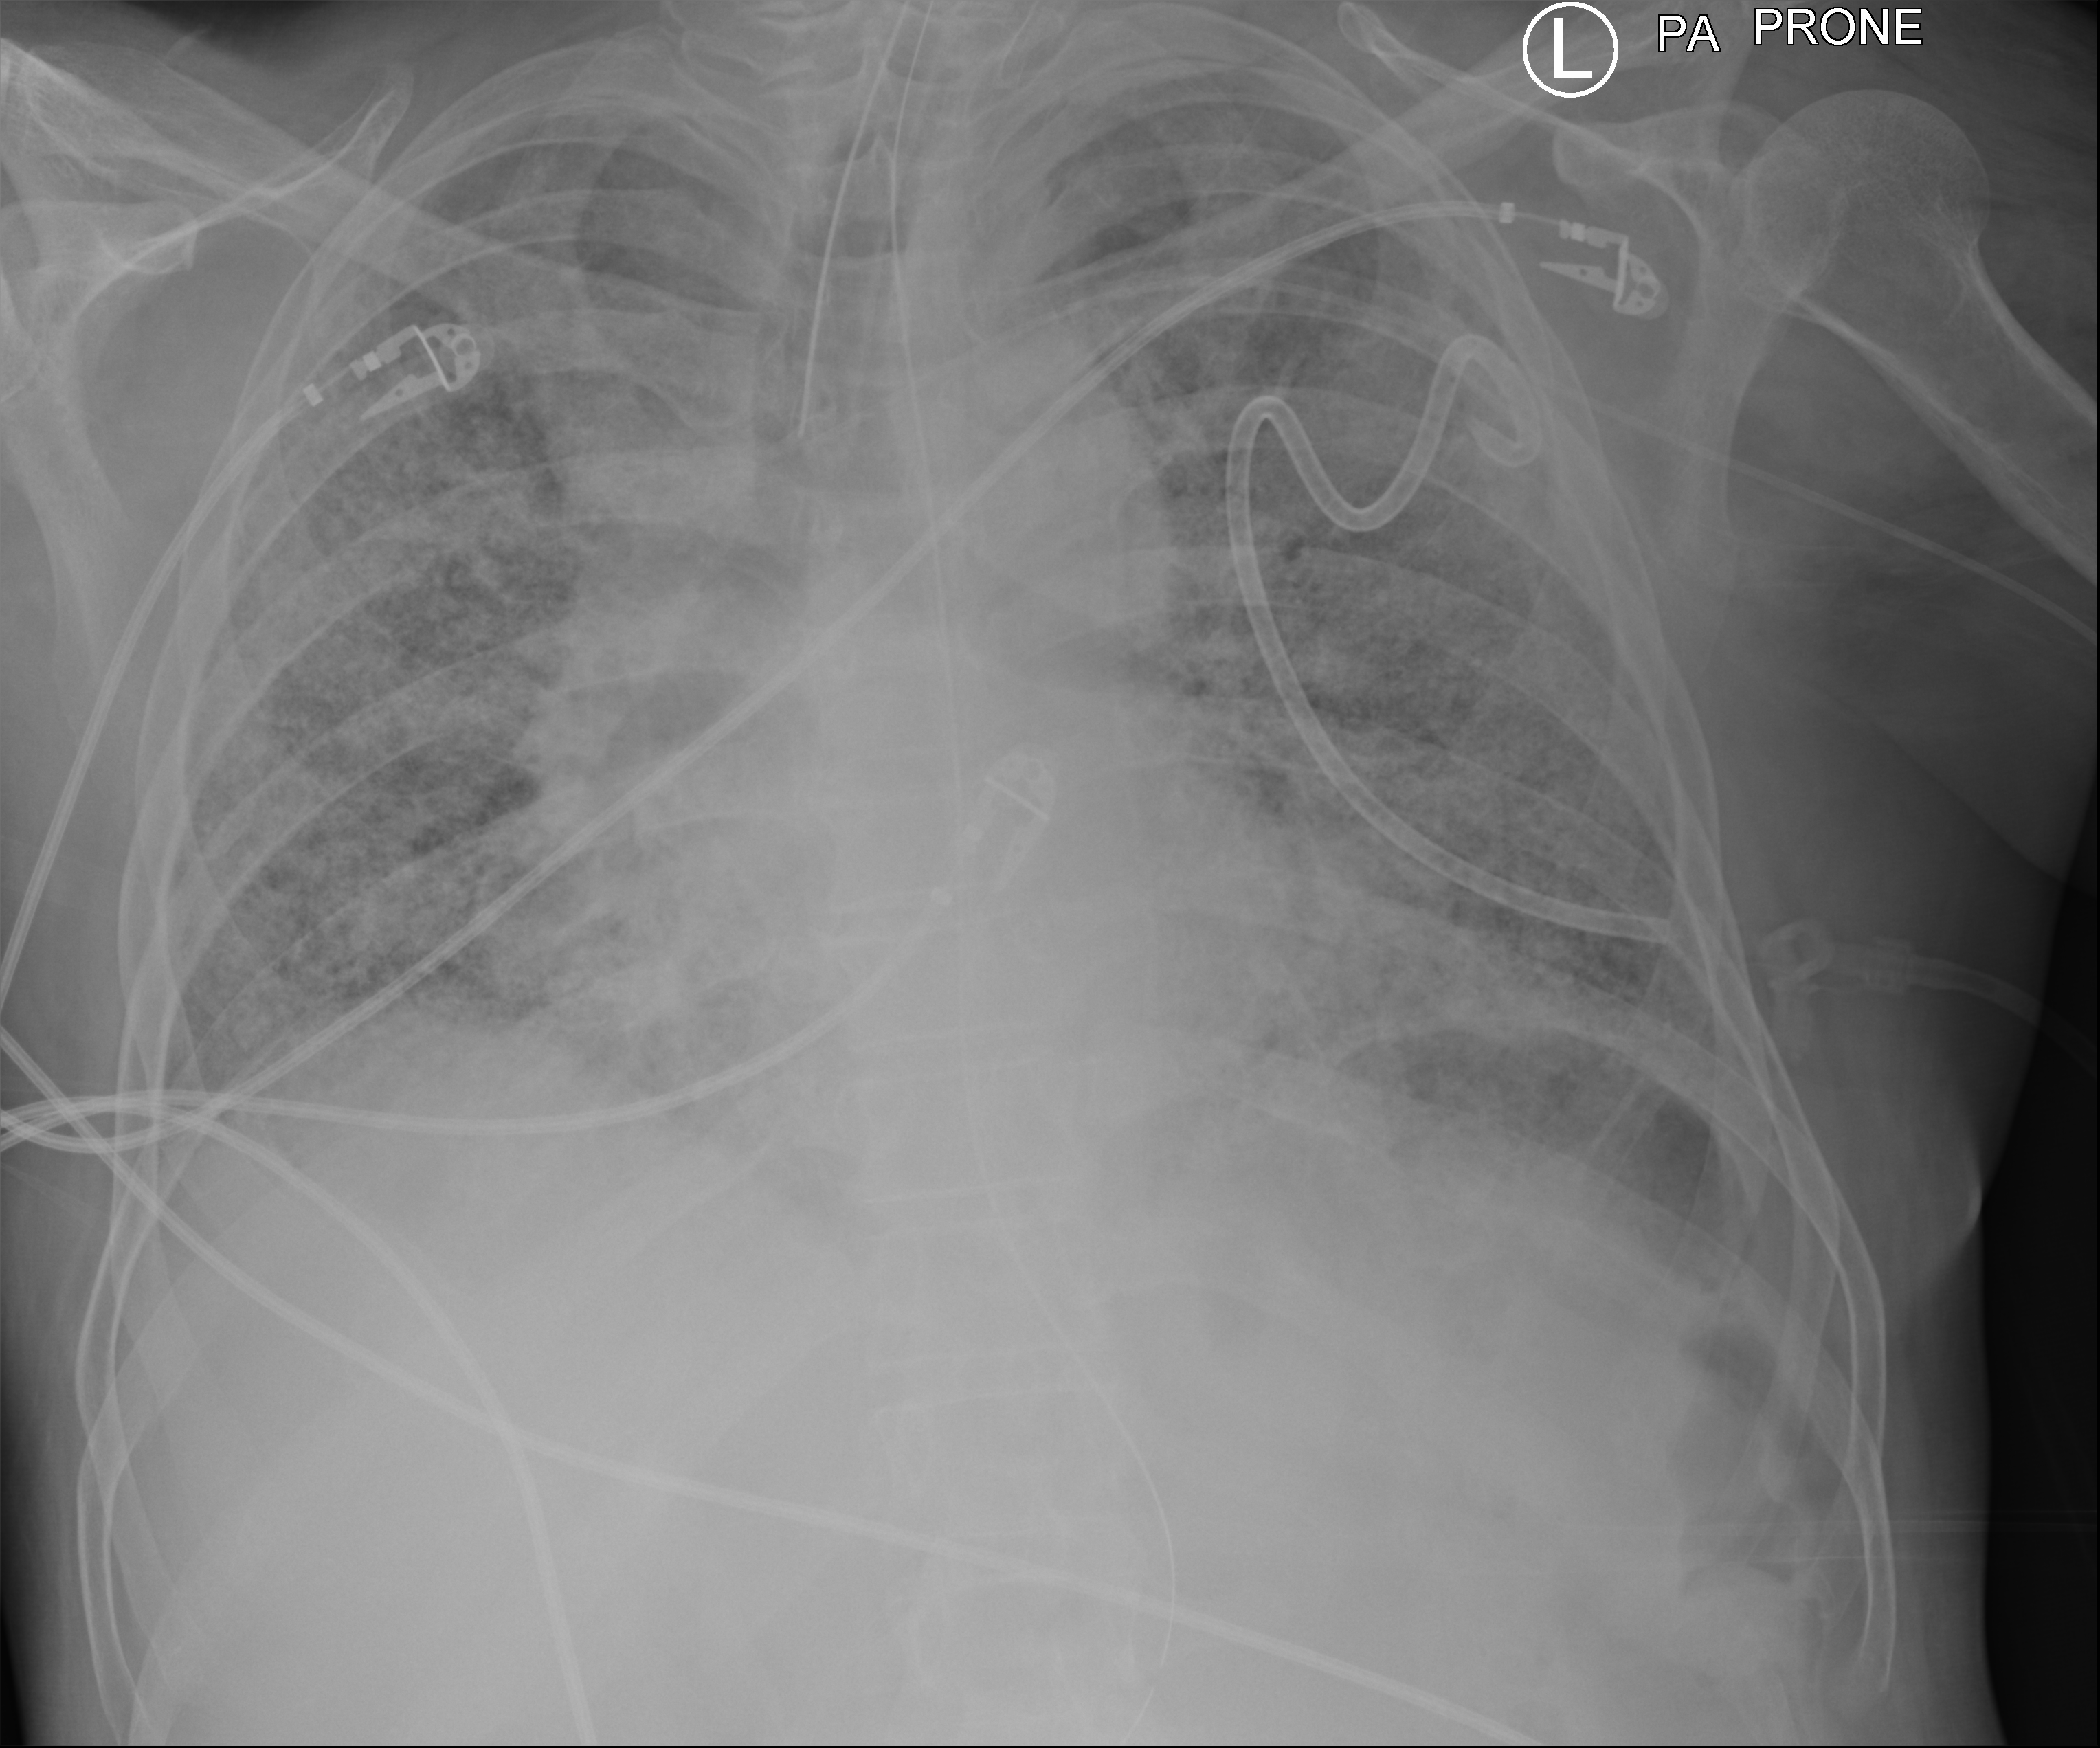
Bedside chest radiograph (computed radiography); posteroanterior (PA) projection. Patient hospitalised with COVID-19; male, aged 60–74 years.
From the hospital-stay record, not from the radiograph (when in the stay this image was taken is not recorded): mechanically ventilated during this hospital stay: yes; admitted to intensive care during this hospital stay: yes; length of hospital stay: 54 days.